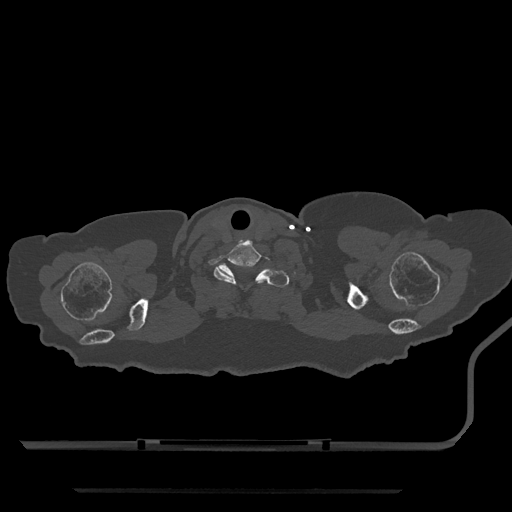
CT including the spine, one axial slice. Position 727 of 797 along the scan axis. Reconstruction kernel Br40s/3. Bone window (W 1800 / L 400 HU). 0.5 mm slice thickness. 512 × 512 image matrix, field of view 440 × 440 mm. Patient: female, 51 years. From the clinical record (not read from this slice): primary cancer: neuro.
Annotated regions visible in this slice (semi-automatically segmented with operator editing):
- T1 vertebra: bounding box <218,264,290,287> (left, top, right, bottom; pixels)